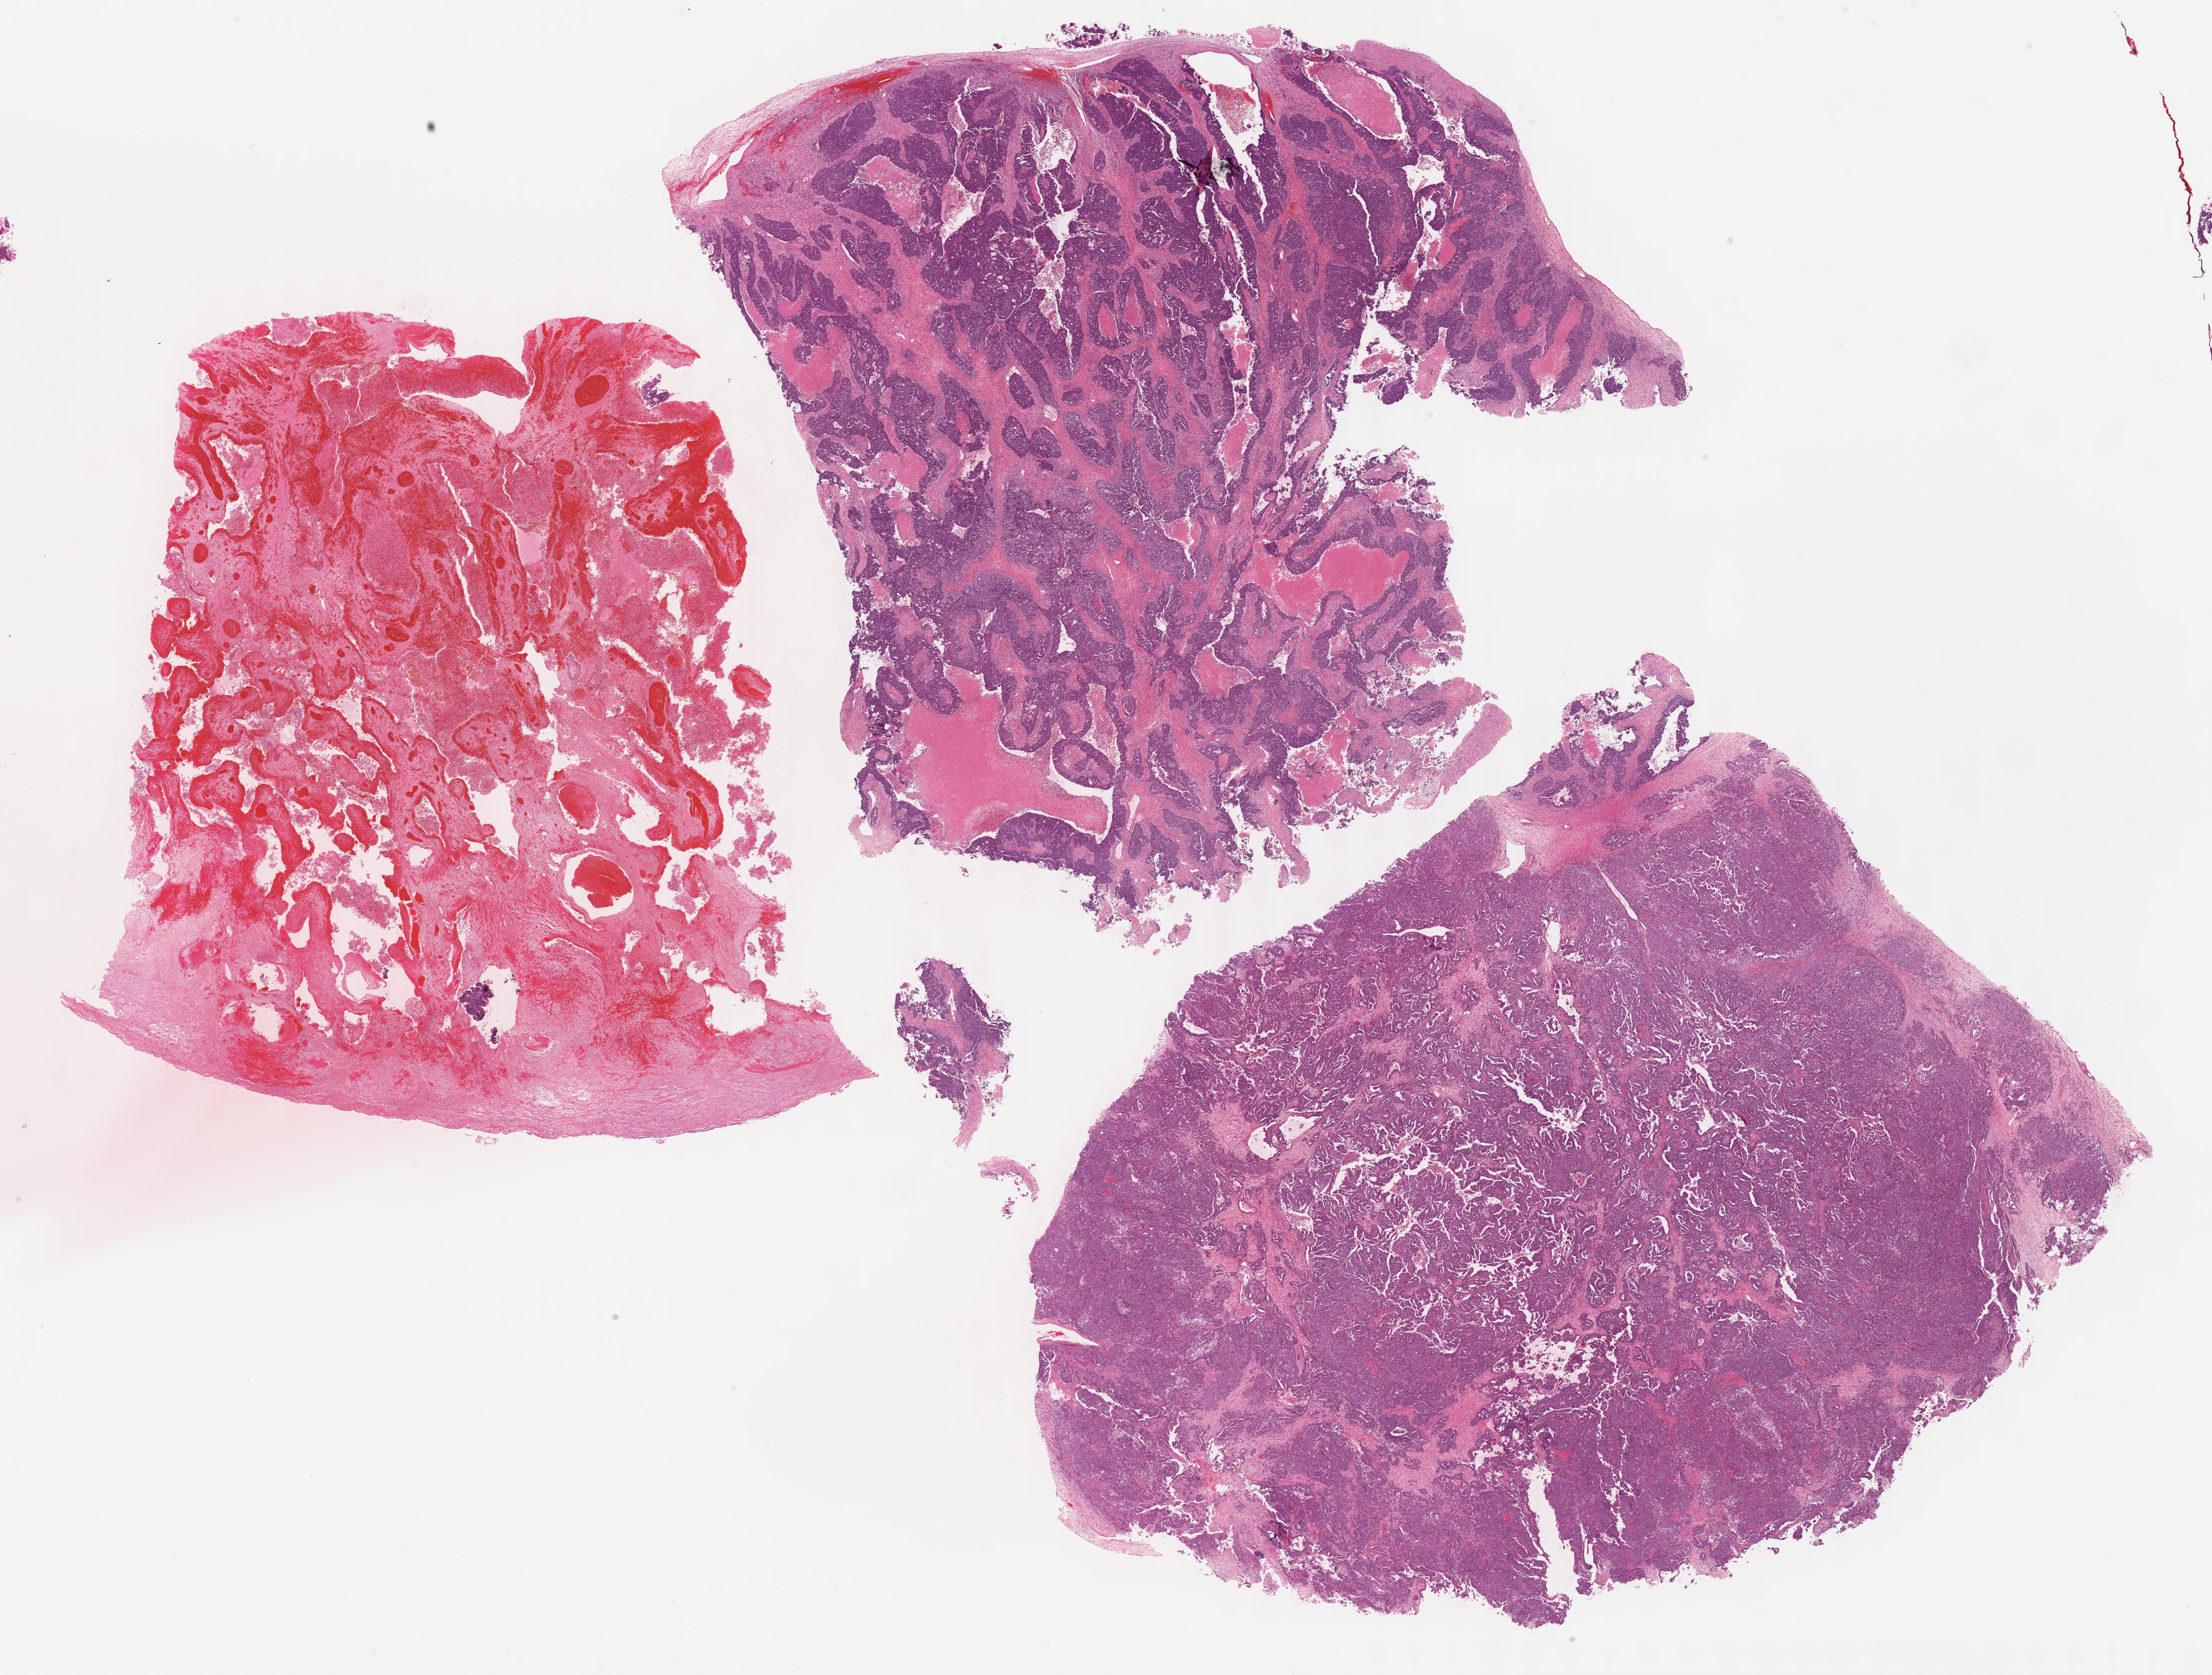
Hematoxylin and eosin (H&E) stained whole-slide image, whole scanned area (about 28.7 x 21.7 mm) shown as a low-resolution overview, formalin-fixed paraffin-embedded (FFPE) diagnostic section, sample: primary tumour, ovary. Patient: female, age at initial diagnosis 54 years. Histologic grade: G3 (poorly differentiated).
FIGO stage: IIIC. Pathologic diagnosis: Serous cystadenocarcinoma, NOS.